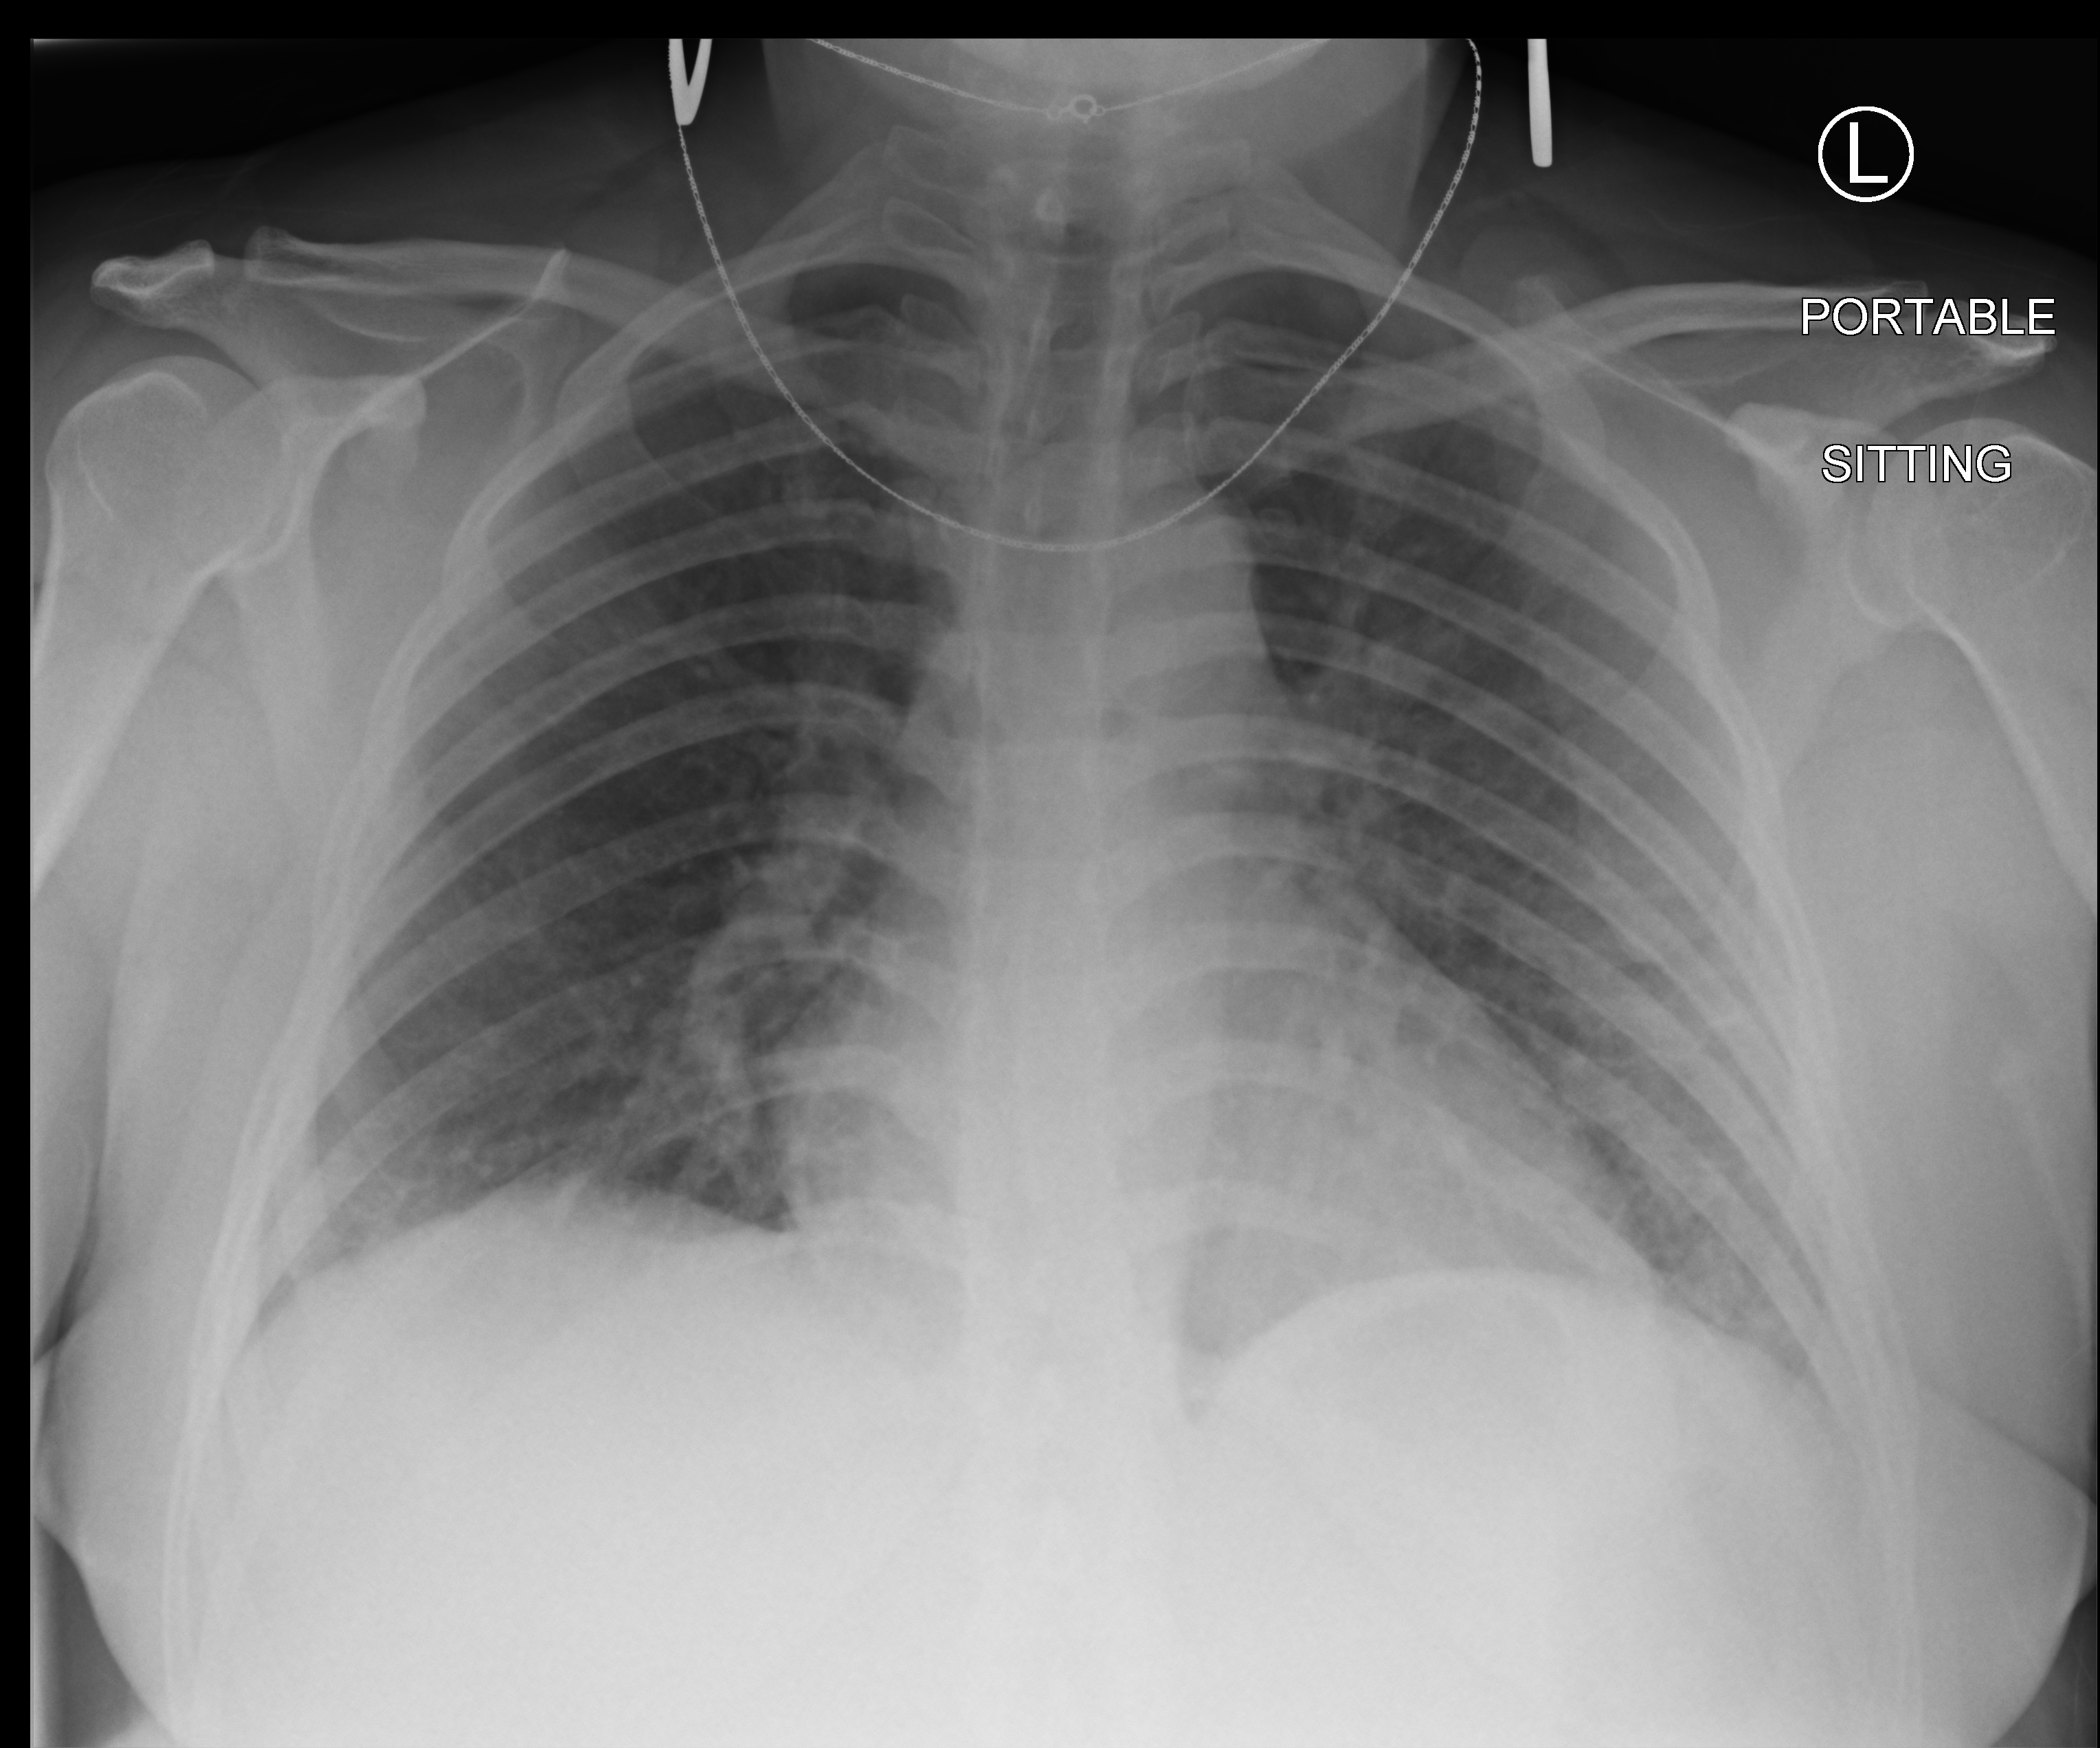
Bedside chest radiograph (computed radiography), anteroposterior (AP) projection. Female patient hospitalised with COVID-19, age 18–59 years.
Admission-level facts for this patient (not findings on this image; timing relative to this image not recorded): mechanically ventilated during this hospital stay: no; admitted to intensive care during this hospital stay: no; chronic kidney disease (admission record): no.